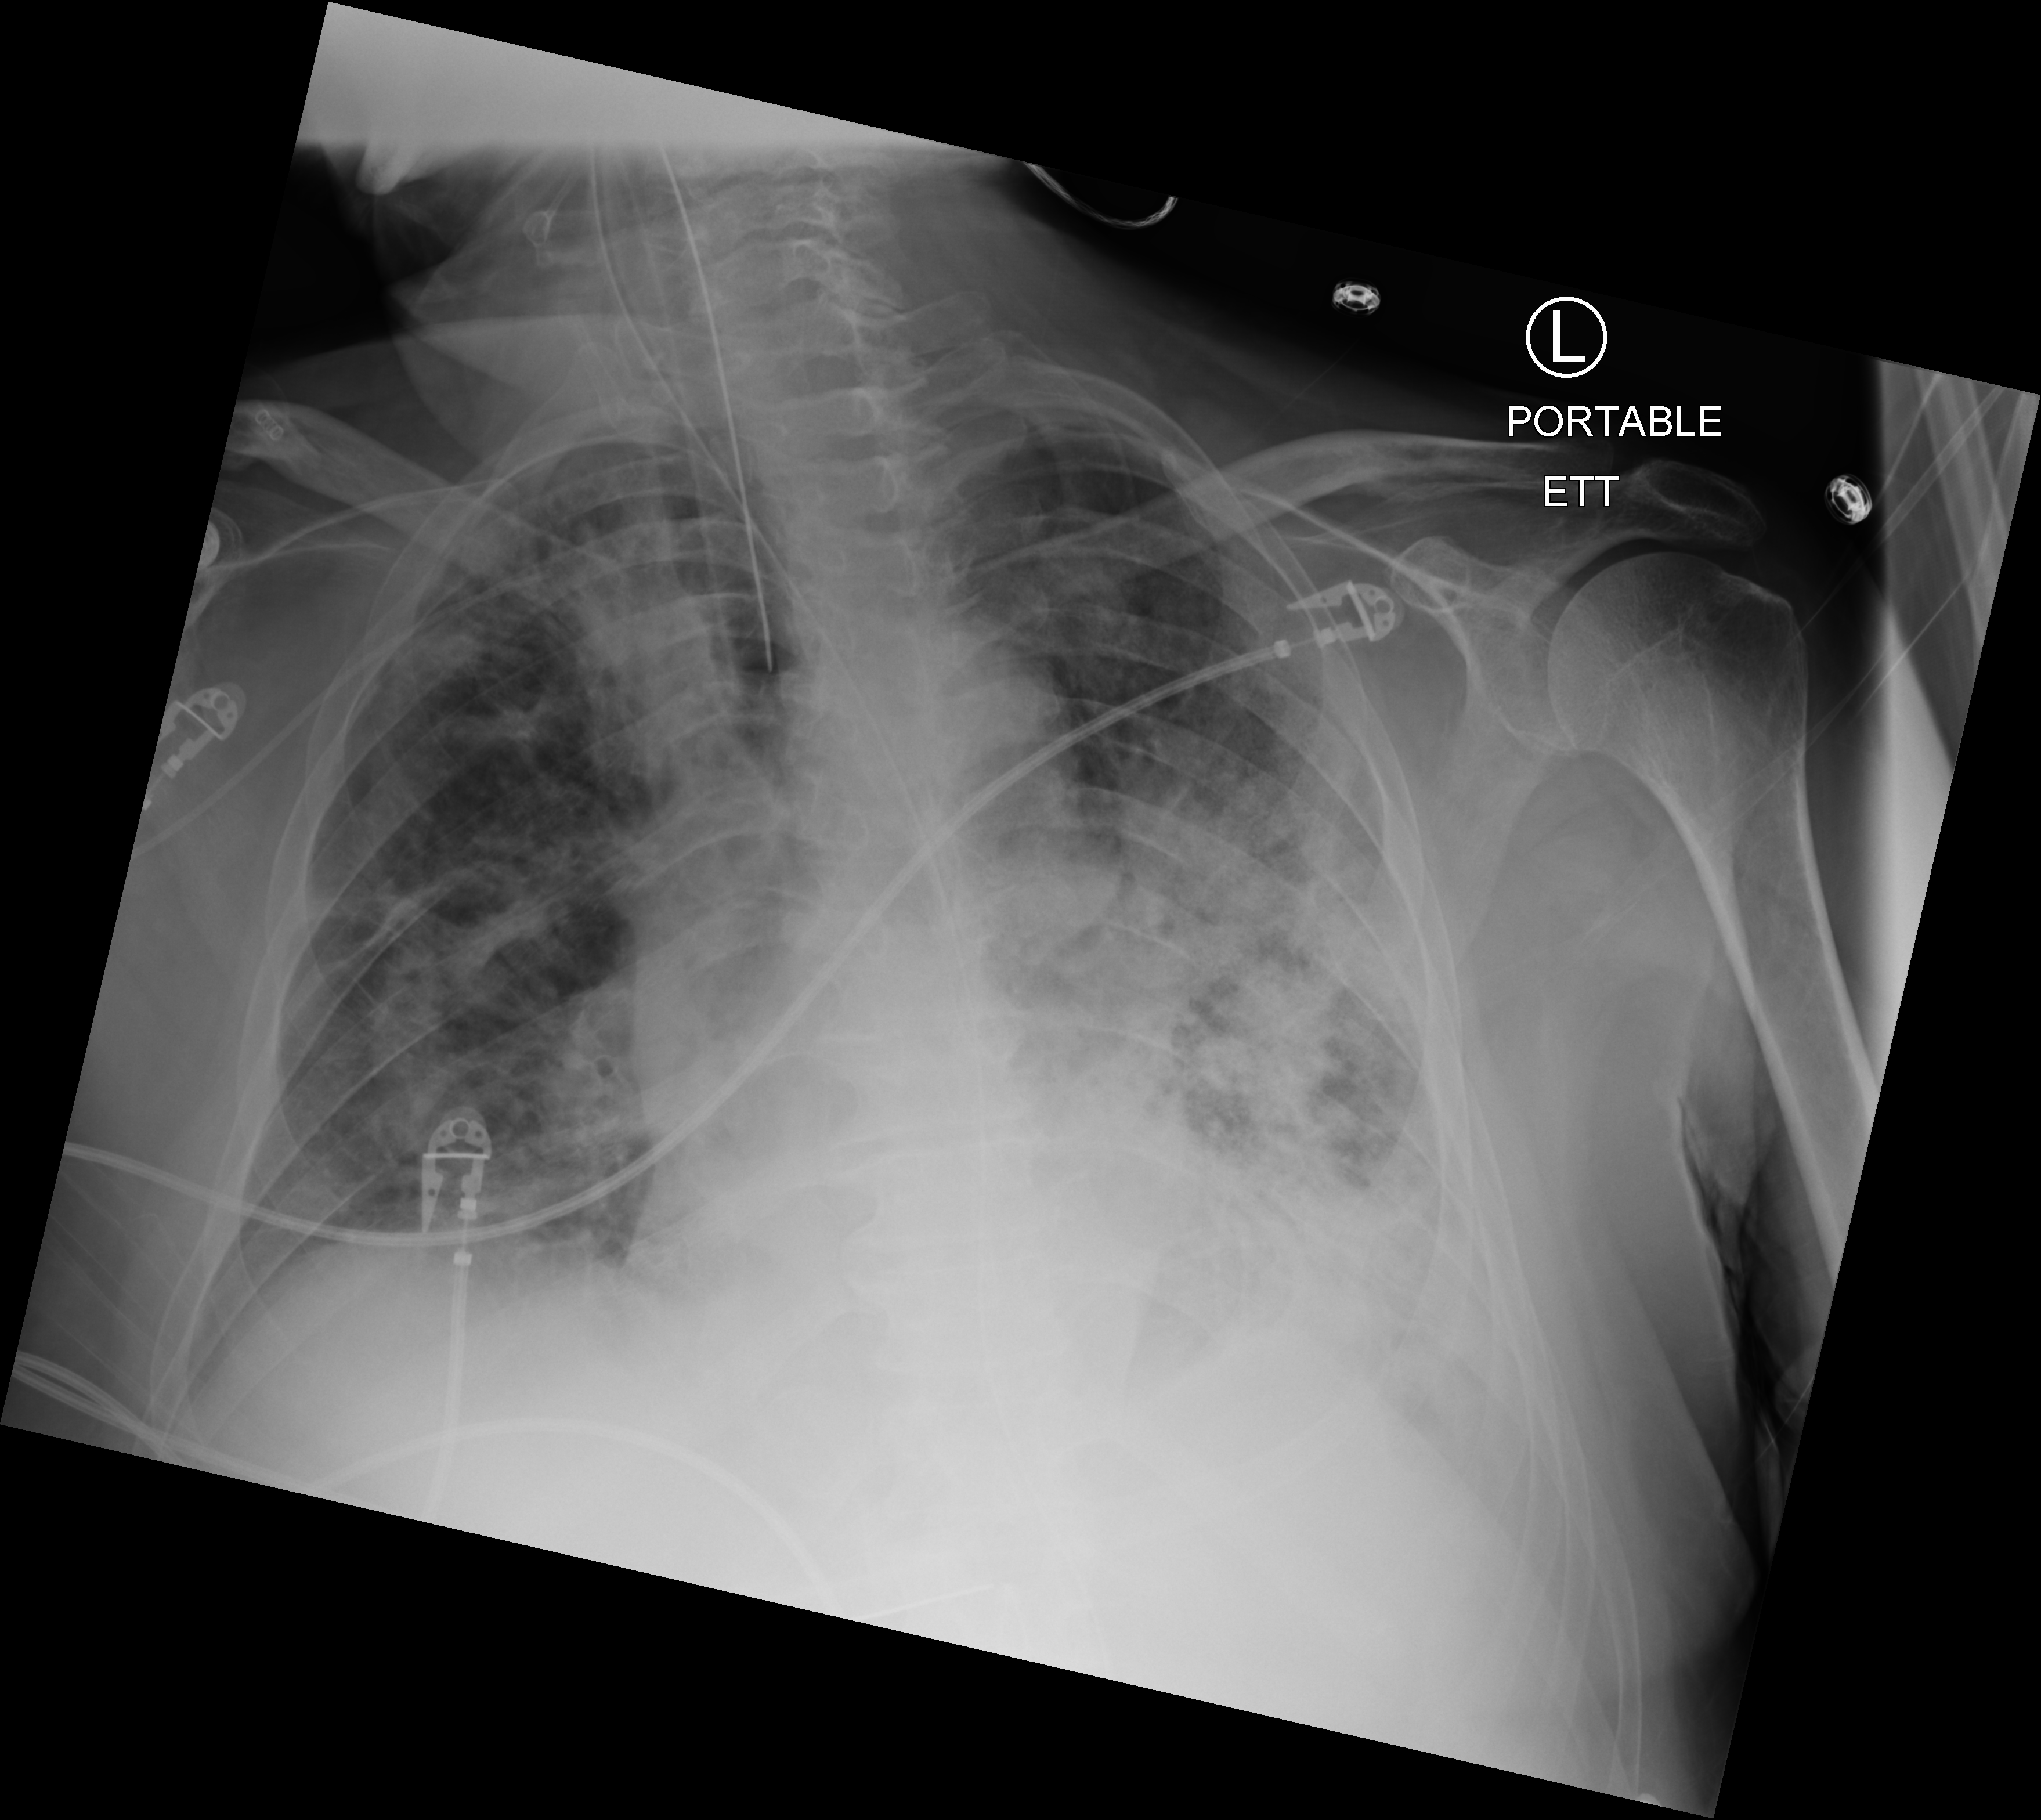
Chest X-ray (portable), anteroposterior (AP) projection. Patient hospitalised with COVID-19; male, aged 60–74 years.
Hospital-stay facts (about this admission, not read from this image; timing relative to this image not recorded):
- length of hospital stay: 24 days